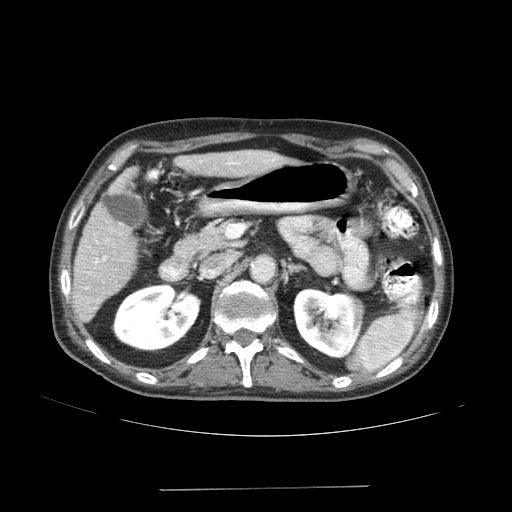
Contrast-enhanced abdominal CT (liver protocol), one axial slice; position 76 of 192 along the scan axis; 120 kVp; soft-tissue window (W 400 / L 40 HU); 512 × 512 image matrix. Case-level facts recorded for this patient, not image findings: diagnosis: hepatocellular carcinoma (patient treated with transarterial chemoembolisation; whether this scan precedes or follows treatment is not stated here); TNM stage (as recorded): Stage-IVA; Child-Pugh class: A; tumour differentiation: poorly differentiated.
Annotated regions visible in this slice (semi-automatically segmented with operator editing):
- liver parenchyma outside the tumour (the mass and vessels are separate outlines, so this box may not span the whole liver): bounding box (x1, y1, x2, y2) in pixels: (72, 150, 286, 322)
- liver vessels: (96, 162, 236, 262)